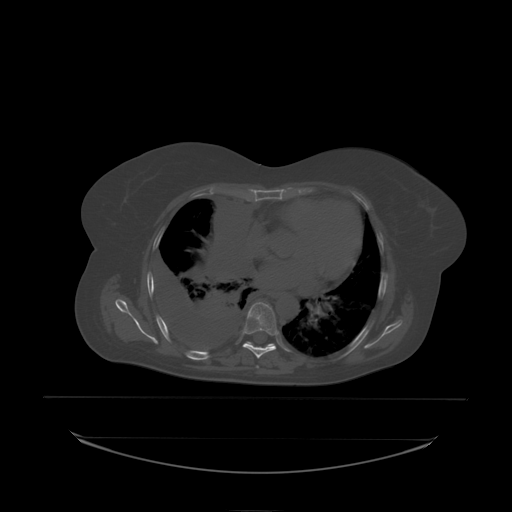
CT including the spine, one axial slice. Position 140 of 242 along the scan axis. Bone window (W 1800 / L 400 HU). 2.5 mm slice thickness. 512 × 512 image matrix, field of view 500 × 500 mm. Female patient, age 53 years. From the clinical record (not read from this slice): primary cancer: lung.
Annotated regions visible in this slice (semi-automatic segmentation, software-assisted and operator-edited):
- T7 vertebra: bounding box (x1, y1, x2, y2) in pixels: (243, 302, 278, 336)